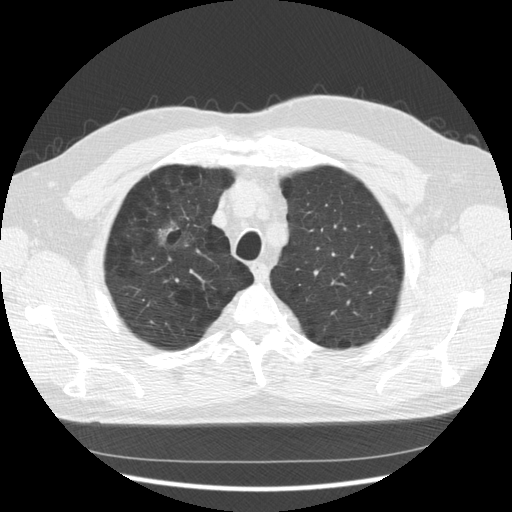
Chest CT (low-dose screening protocol), one axial image, third annual screen, lung window (W 1500 / L -600 HU), standard (soft-tissue) reconstruction kernel (STANDARD), slice 102 of 133 in the series, 512 × 512 image matrix. Male, age 60 years at enrolment. Former smoker at enrolment.
Expert reader's lesion annotation, bounding box (x1, y1, x2, y2) in pixels: (143, 208, 198, 265). The exam's reader record, not a measurement of the box and not confirmed to be the same lesion: non-calcified nodule or mass ≥4 mm, right upper lobe, poorly defined margins, mixed attenuation, pre-existing on the prior screen: yes; interval growth: yes.